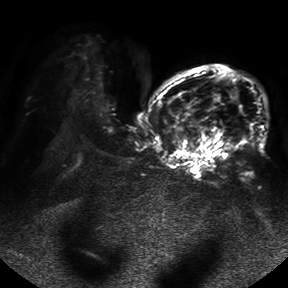
Breast MRI, one axial slice; position 27 of 50 along the scan axis; diffusion-weighted series; image 2 of 4 stored at this slice position (different b-values; order by instance number); 1.5 T; 288 × 288 image matrix, field of view 390 × 390 mm. Female patient.
Annotated regions visible in this slice (outlined manually by an expert reader):
- tumour on diffusion-weighted imaging: bounding box (x1, y1, x2, y2) in pixels: (225, 90, 238, 148)